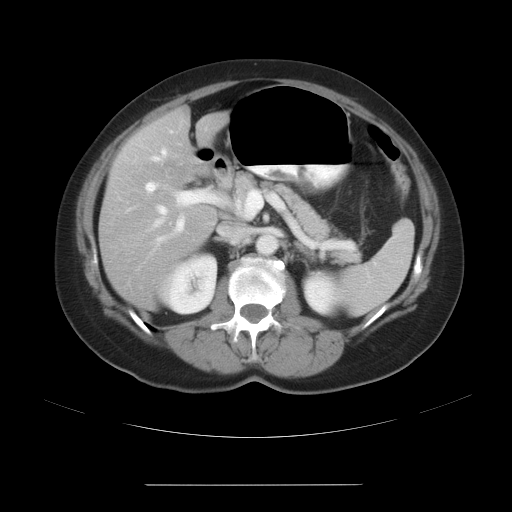
Contrast-enhanced abdominal CT, one axial slice; position 15 of 27 along the scan axis; reconstruction kernel STANDARD; intravenous contrast given; soft-tissue window (W 400 / L 40 HU); 512 × 512 image matrix, field of view 440 × 440 mm. Female patient, age 58 years. Case-level facts recorded for this patient, not image findings: diagnosis: colorectal cancer liver metastases, imaged before liver resection; multiple liver metastases: yes; largest metastasis: 1.9 cm; chemotherapy before resection: yes.
Structures marked on this image (manually delineated by an expert):
- hepatic veins: bounding box [x1, y1, x2, y2] px = [143, 148, 172, 236]
- liver: [99, 110, 220, 306]
- planned liver remnant (the part of the liver to remain after resection): [107, 115, 212, 215]
- portal vein (with intrahepatic branches): [112, 128, 254, 271]
- liver metastasis: [182, 108, 189, 116]
- liver metastasis: [184, 110, 190, 116]